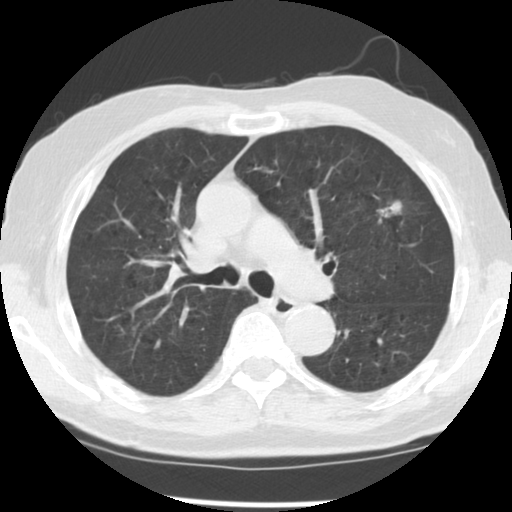
Chest CT (low-dose screening protocol), one axial image; third annual screen; lung window (W 1500 / L -600 HU); standard (soft-tissue) reconstruction kernel (STANDARD); slice 82 of 131 in the series. Male, age 70 years at enrolment. Current smoker at enrolment.
Lesion marked by an expert reader, bounding box (x1, y1, x2, y2) in pixels: (356, 184, 415, 244). The screening reader recorded 3 non-calcified nodules or masses ≥4 mm on this exam; which of them this box marks is not recorded. Later outcome: lung cancer diagnosed 74 days after this screen — adenocarcinoma, NOS, left upper lobe, moderately differentiated (G2), stage IIIA (AJCC 6th edition), 17 mm at pathology.